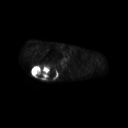
FDG PET of an extremity soft-tissue mass (from a PET/CT study), one axial slice; slice 194 of 267 in the series (ordered by position); 128 × 128 image matrix, field of view 700 × 700 mm. Male patient, age 61 years. Case-level facts recorded for this patient, not image findings: histological type: pleiomorphic spindle cell undifferentiated; grade: high; site of the primary tumour: right parascapusular.
Structures marked on this image (expert contour drawn on MRI and transferred to this co-registered scan by the dataset authors):
- gross tumour volume including surrounding oedema: bounding box (x1, y1, x2, y2) in pixels: (31, 65, 60, 79)
- gross tumour volume (mass): (31, 65, 57, 78)